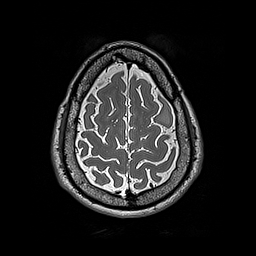
Brain MRI from a brain-tumour surgery series, one axial slice; slice 55 of 192 in the series (ordered by position); 1 mm slice thickness; 256 × 256 image matrix, field of view 250 × 250 mm. Case-level facts recorded for this patient, not image findings: histopathology: Astrocytoma; WHO grade: 2; IDH mutation: yes; tumour location: Left Frontal.
Annotated regions visible in this slice (outlined manually by an expert reader):
- tumour: bounding box <157,107,169,126> (left, top, right, bottom; pixels)